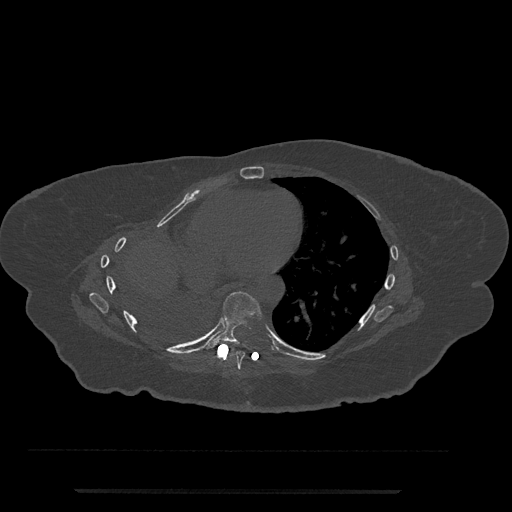
CT including the spine, one axial slice. Slice 409 of 797 in the series (ordered by position). Reconstruction kernel Br40s/3. 120 kVp. Bone window (W 1800 / L 400 HU). 0.5 mm slice thickness. 512 × 512 image matrix, field of view 440 × 440 mm. Female patient, age 51 years. From the clinical record (not read from this slice): primary cancer: neuro.
Annotated regions visible in this slice (semi-automatic segmentation, software-assisted and operator-edited):
- T7 vertebra: bounding box (x1, y1, x2, y2) in pixels: (230, 351, 245, 370)
- T8 vertebra: (206, 291, 262, 349)